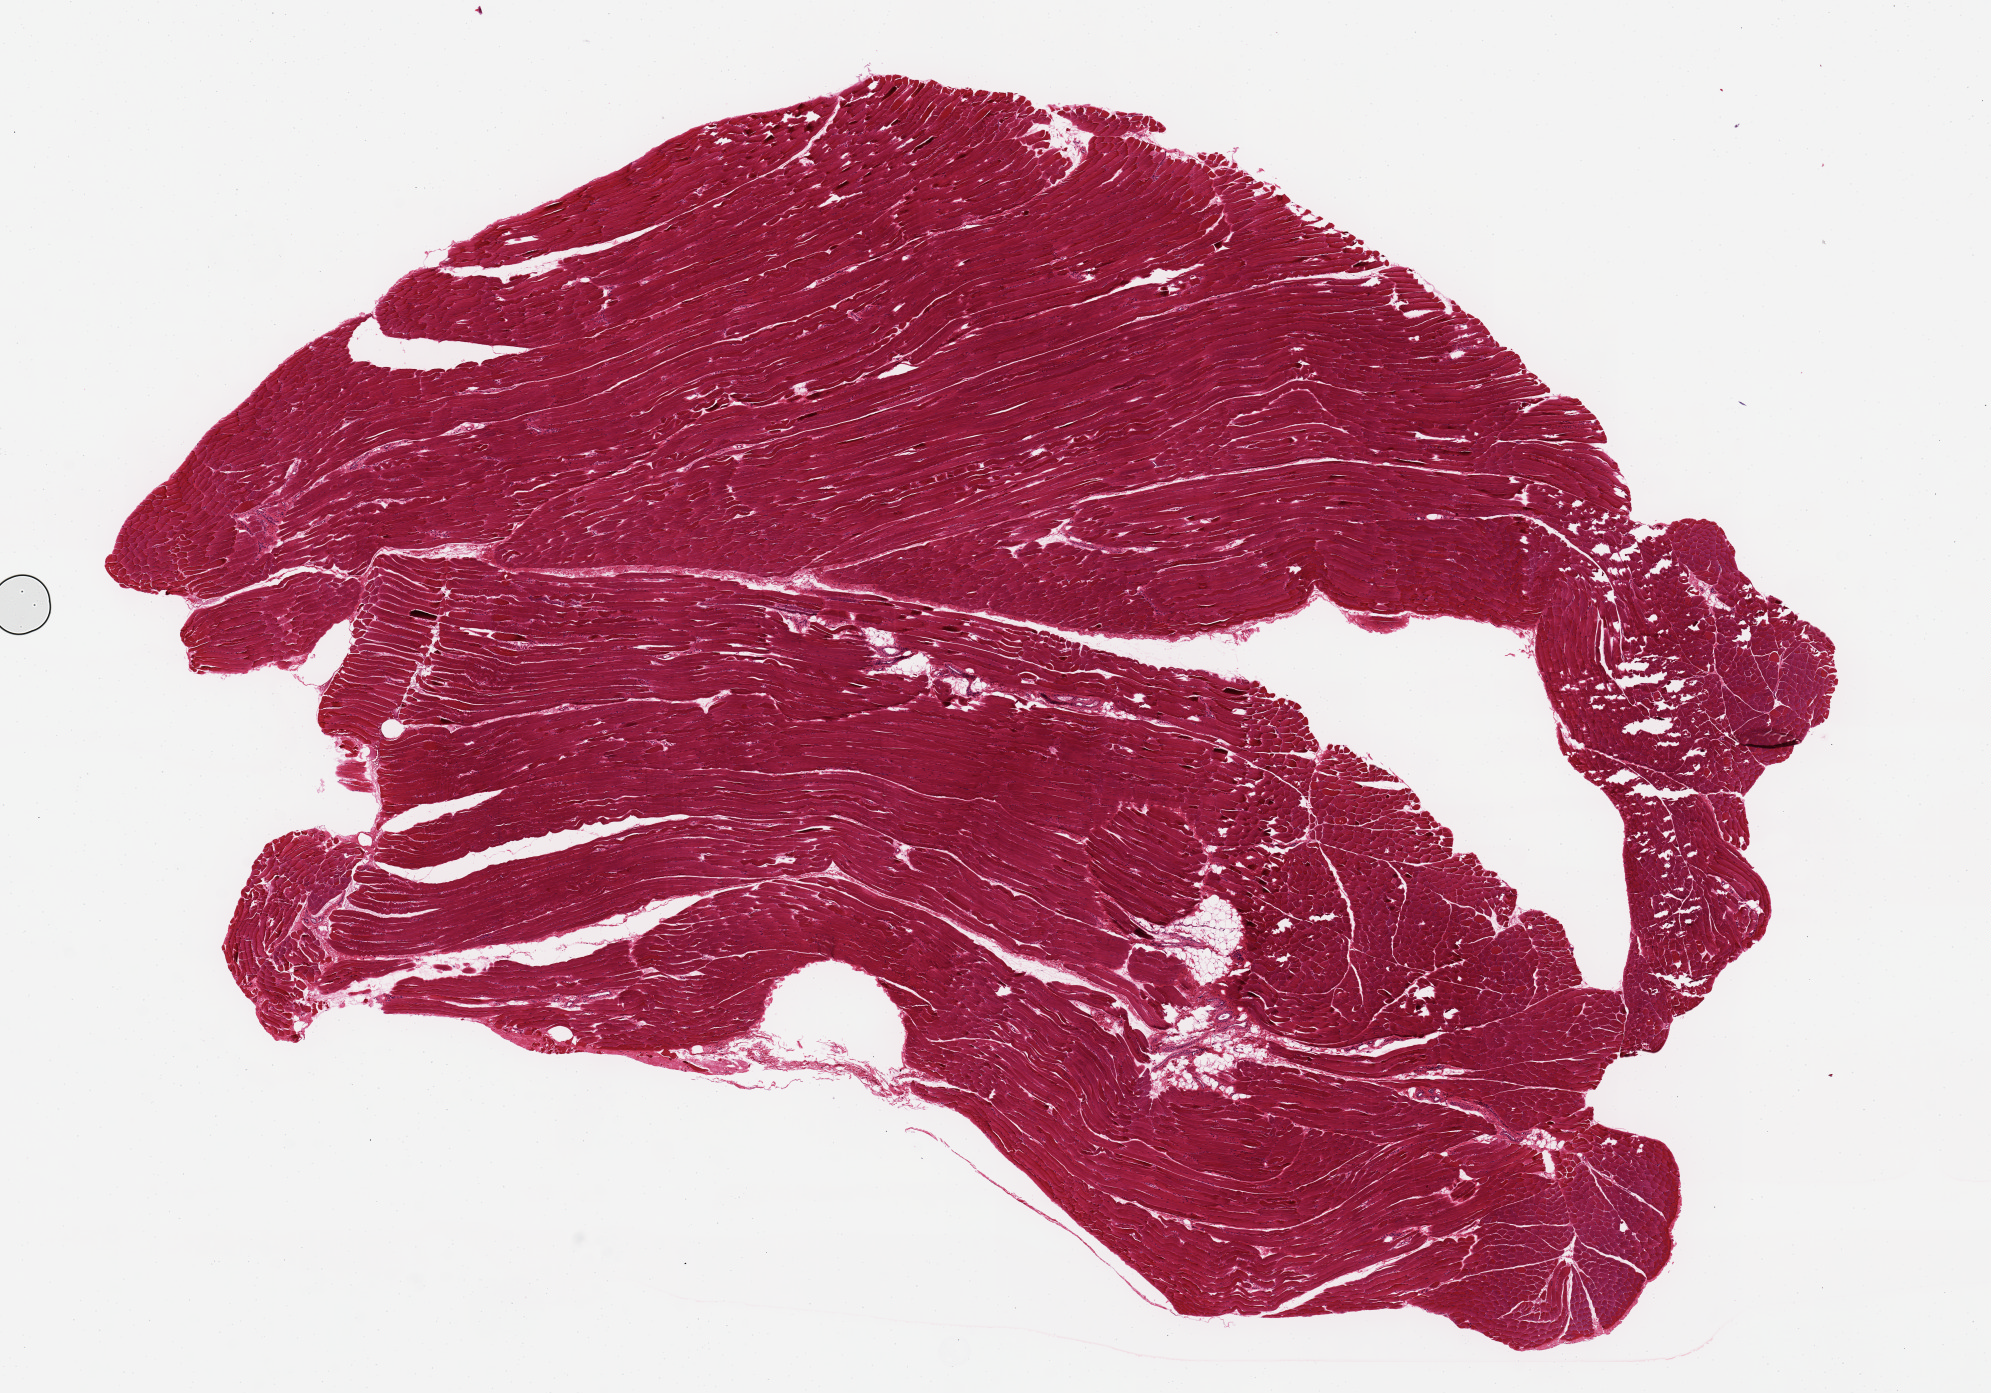
Haematoxylin and eosin whole-slide image, brightfield — low-resolution overview of the scanned area, about 15.8 x 11.0 mm. PAXgene-fixed, paraffin-embedded tissue. Target tissue: skeletal muscle. Donor tissue sample. Male donor.
Reviewer comment on this tissue sample: 1 piece 14x8 mm.